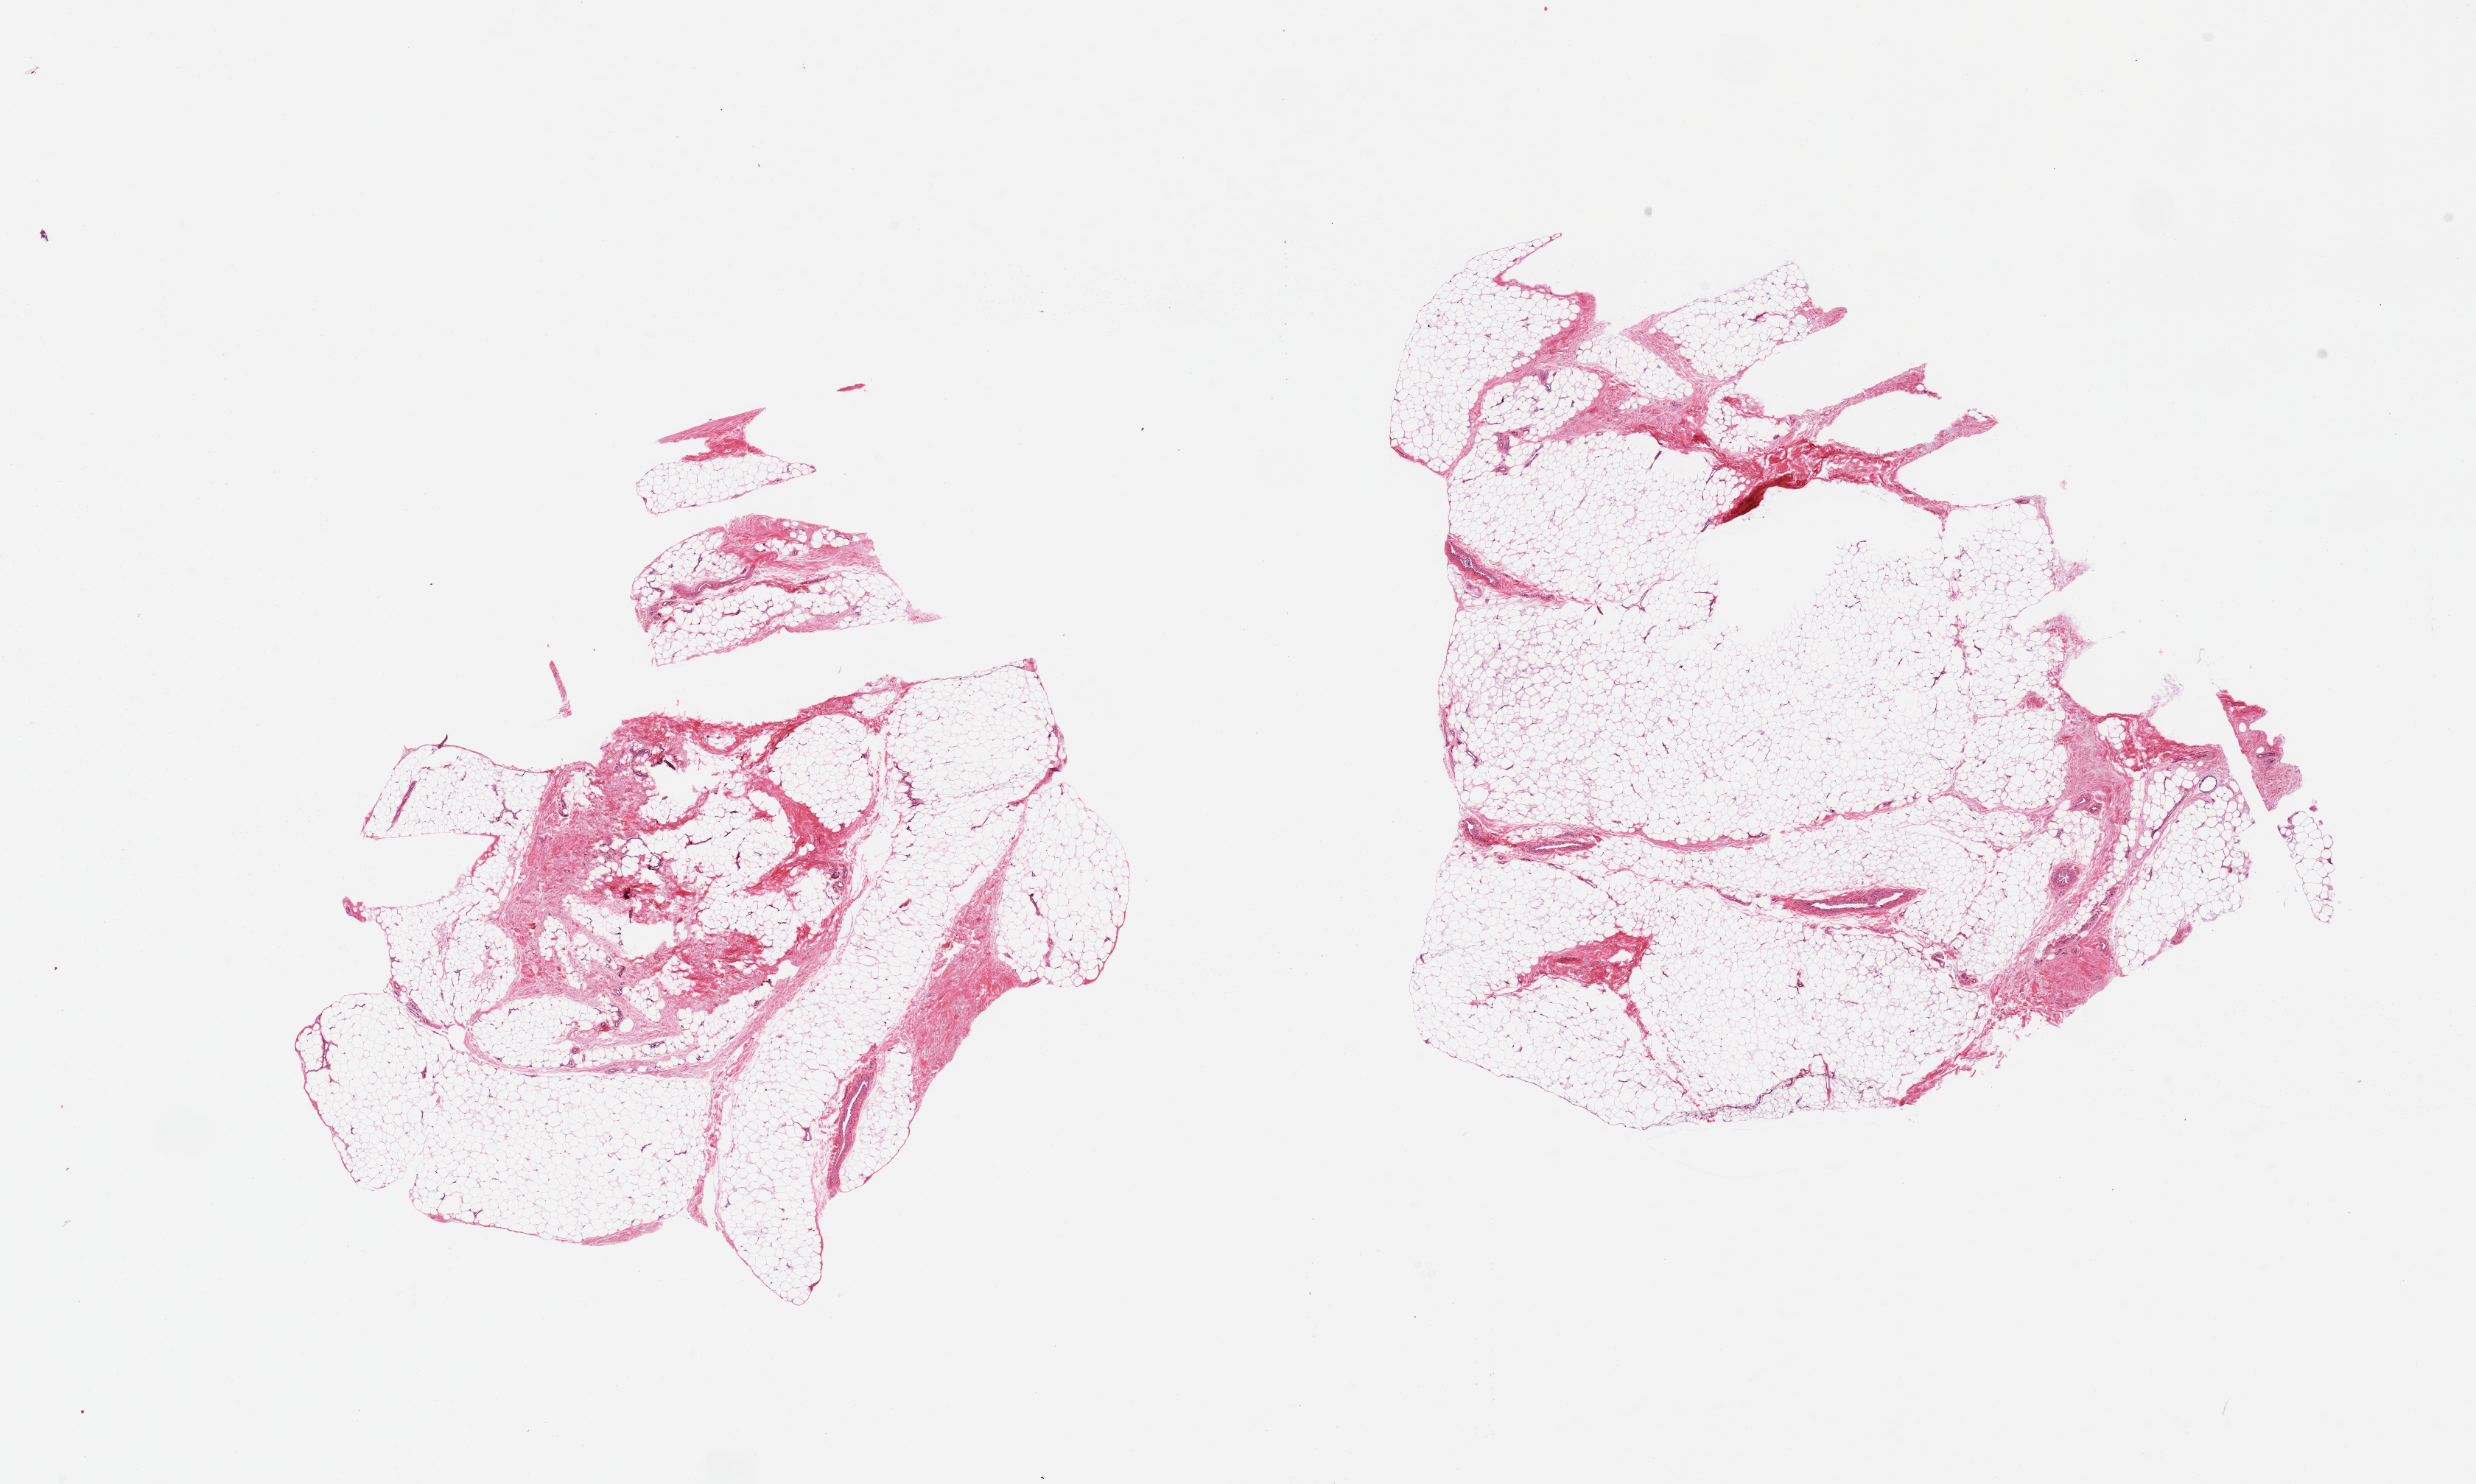
H&E whole-slide image, brightfield — a low-resolution overview of the entire scanned area, about 26.6 x 15.9 mm (from a 20x scan), PAXgene-fixed, paraffin-embedded tissue, section of adipose tissue (target tissue), donor tissue sample. Male donor.
Review note (as recorded): 2 pieces; fat with 10-20% fibrous tissue.